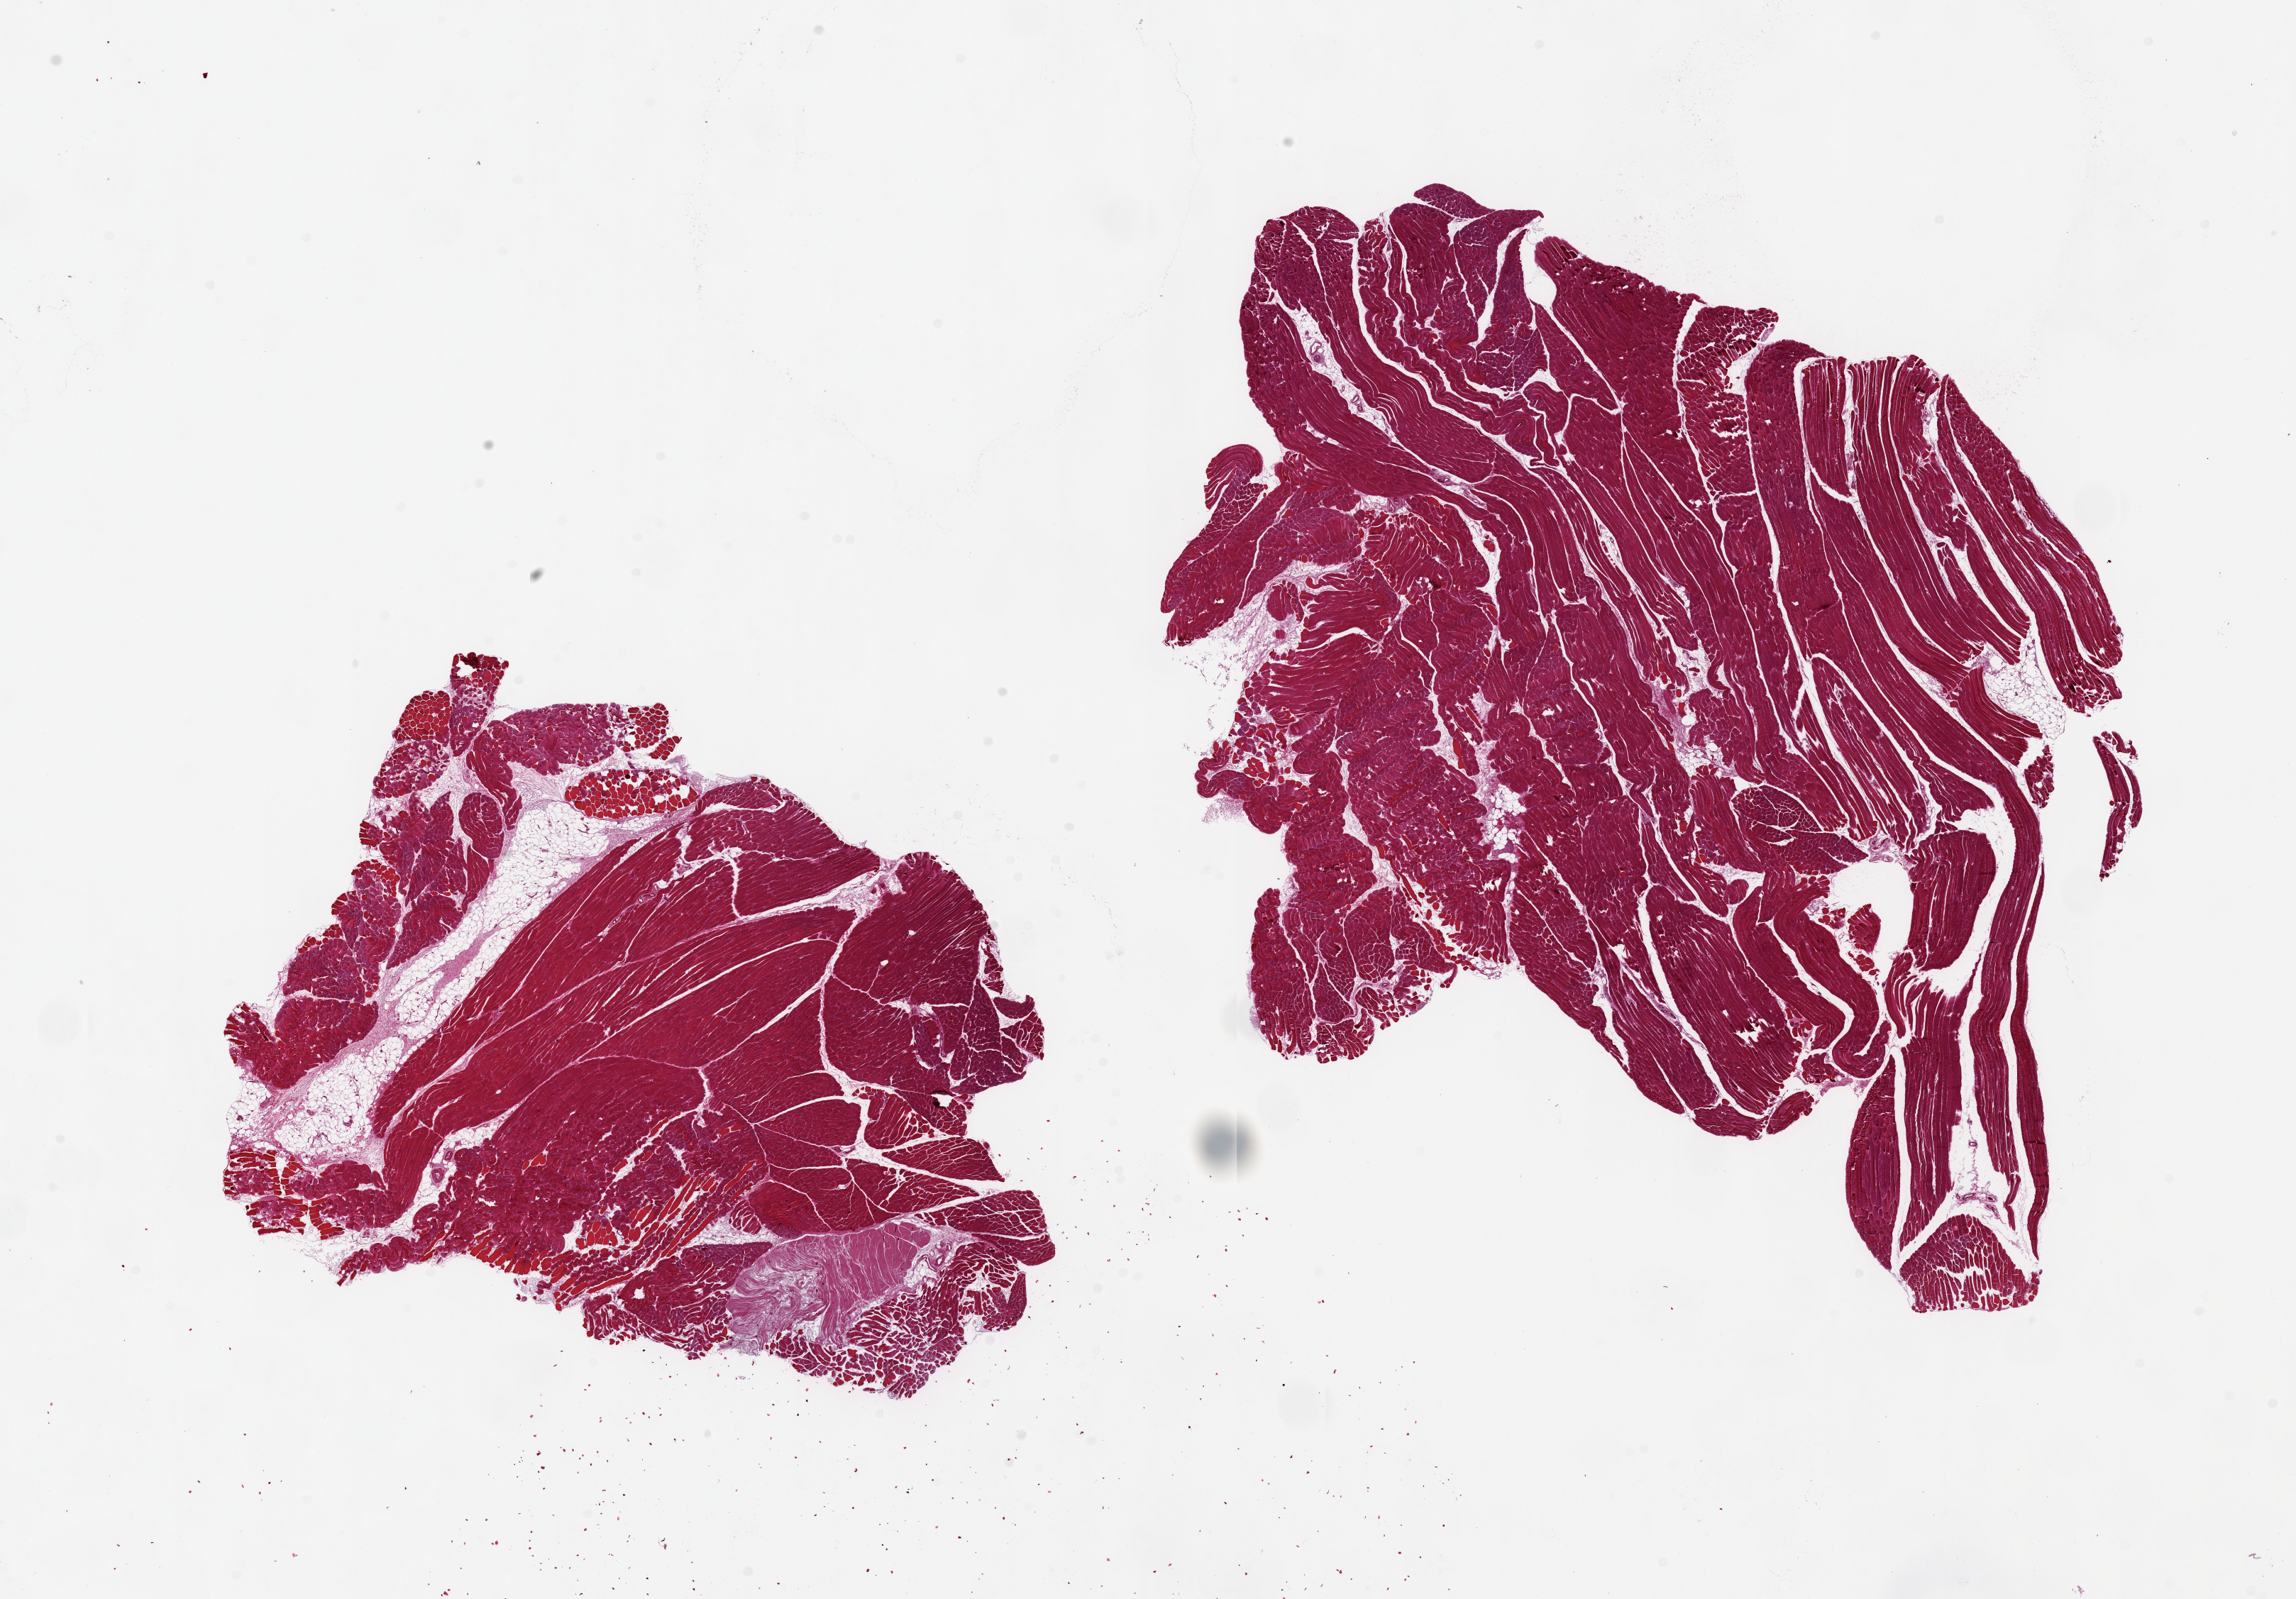
Hematoxylin and eosin (H&E) whole-slide image — whole scanned area (about 25.6 x 17.8 mm) shown as a low-resolution overview; PAXgene-fixed paraffin-embedded (PFPE) section; section of skeletal muscle (target tissue); donor tissue sample.
* reviewer comment on this tissue sample: 2 pieces, 10x8 & 14.5x10.5mm; 2.5x1 mm tendon in small piece along with 10% internal adipose